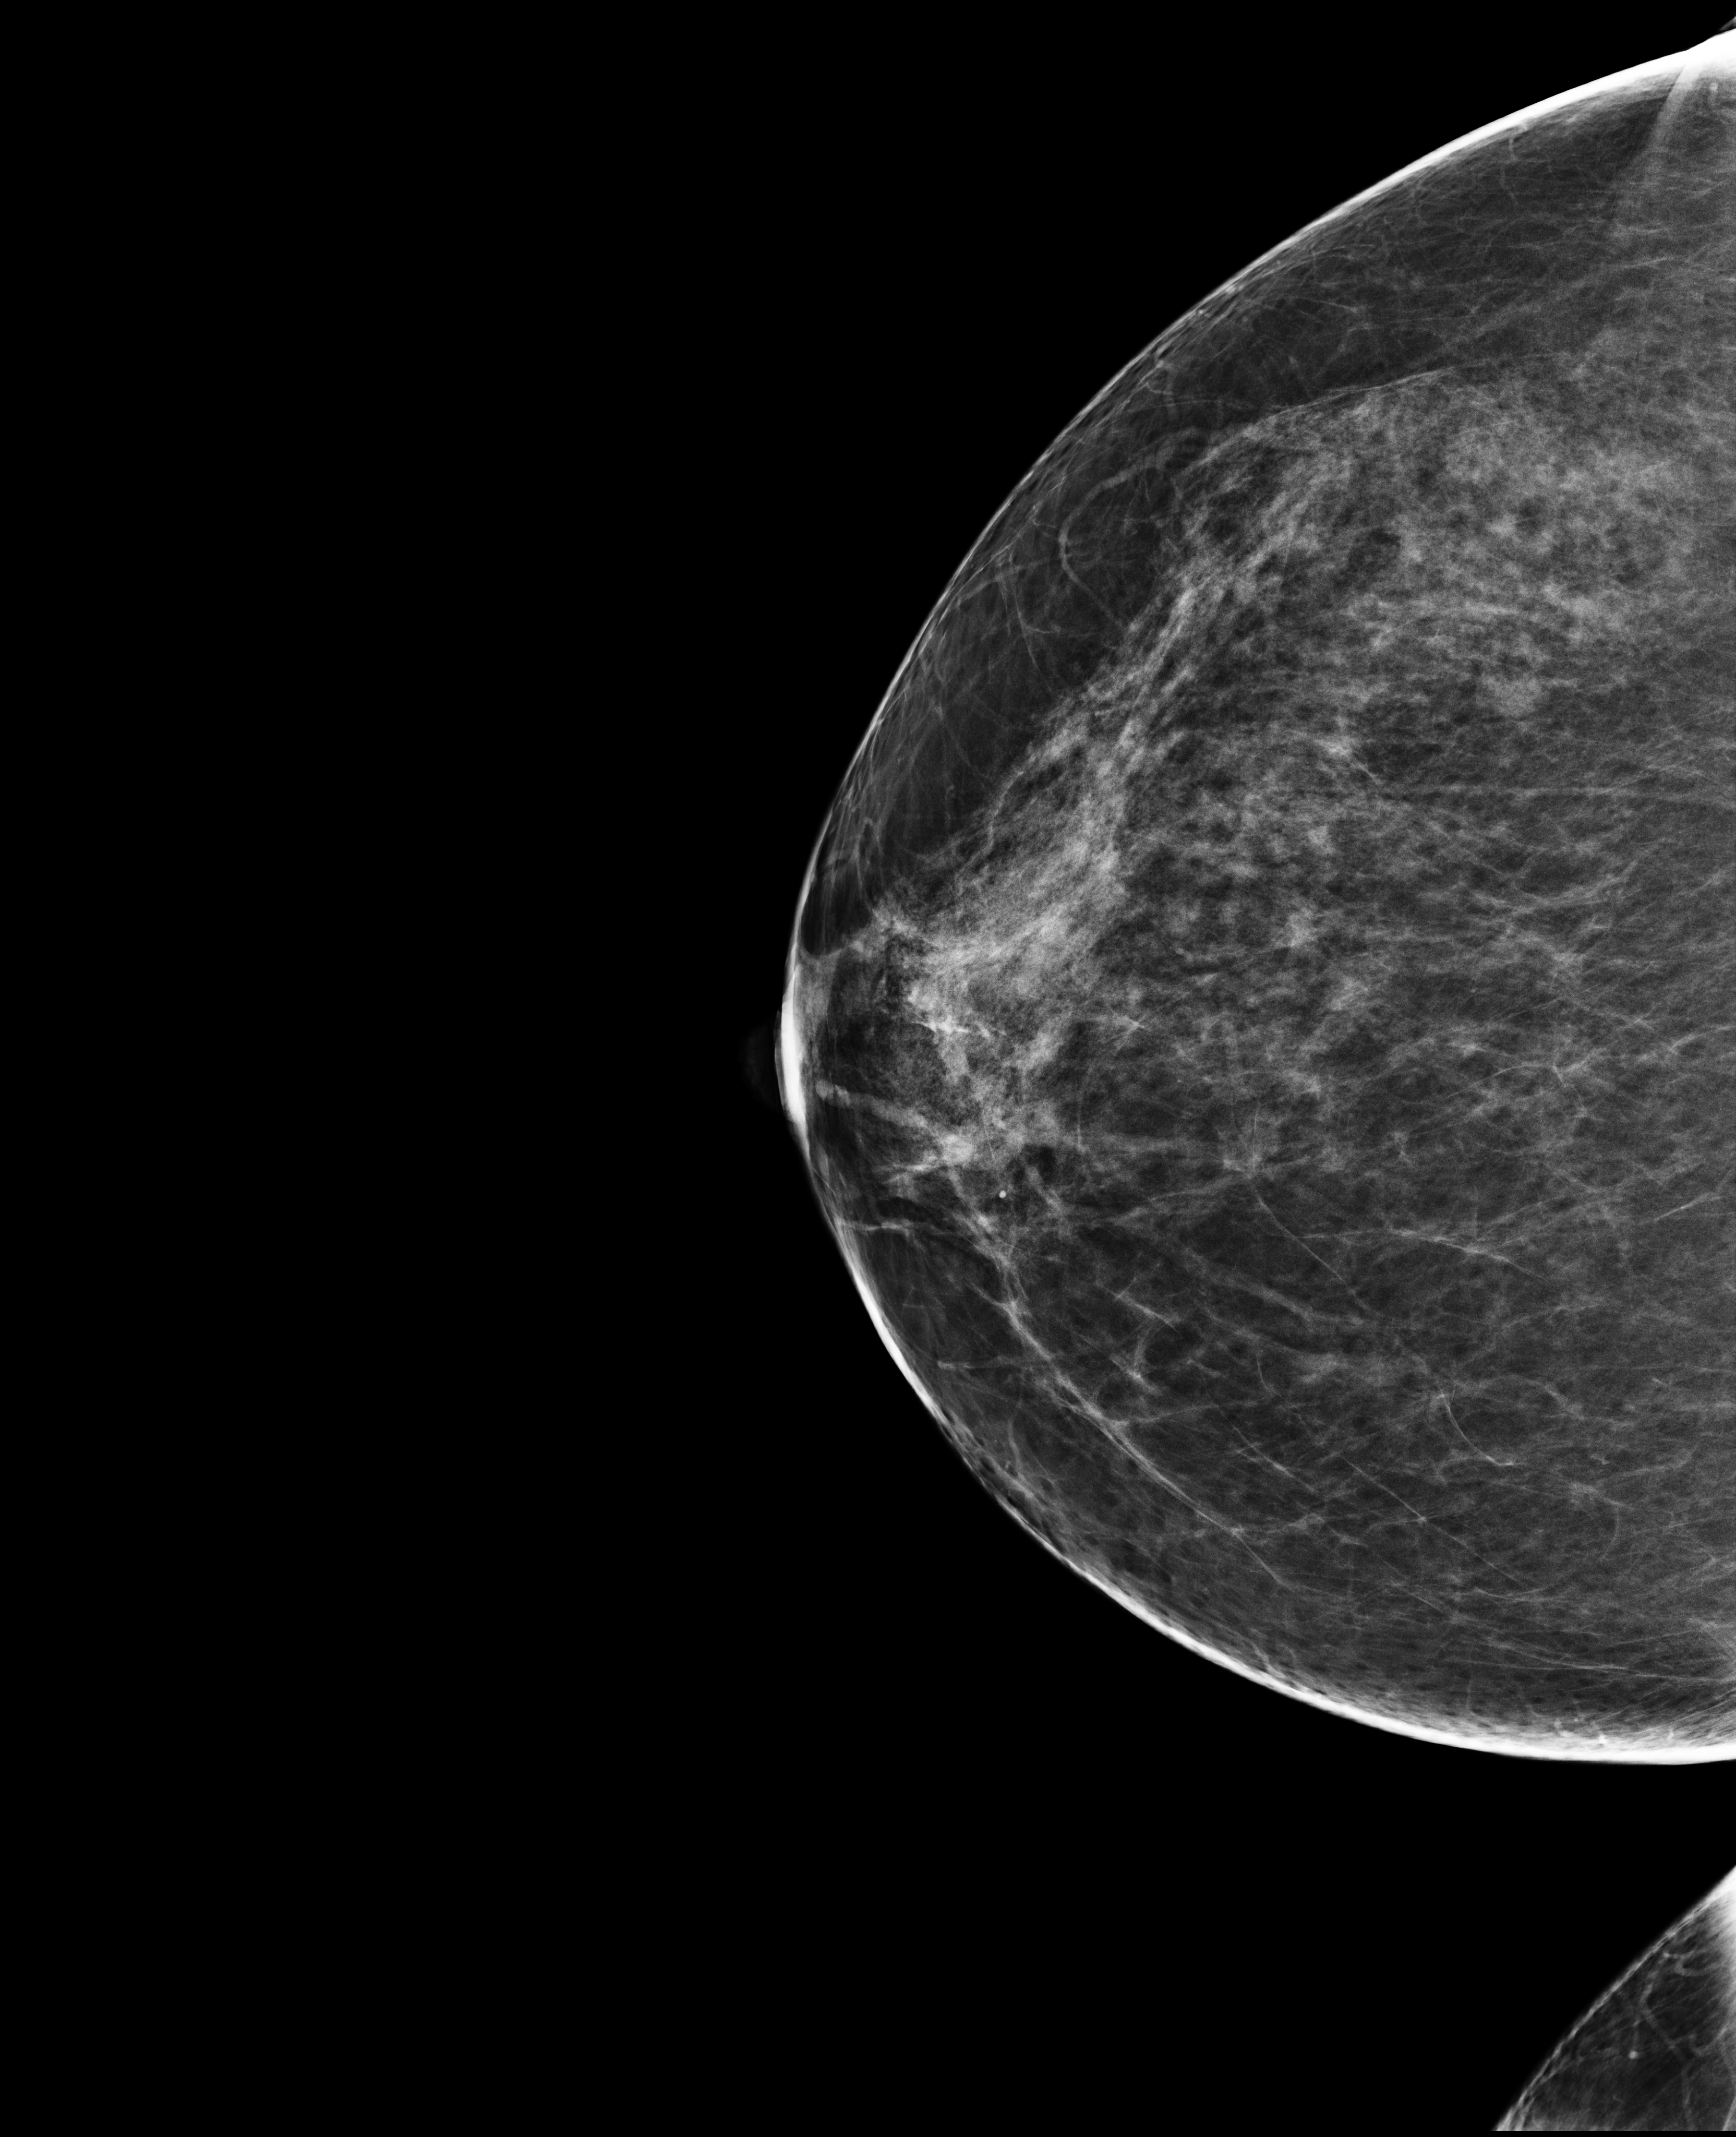
Screening examination; compressed breast thickness 69 mm. Female patient, age 48 years.
Image type: full-field digital mammogram. Breast: right. Projection: craniocaudal (CC) view.